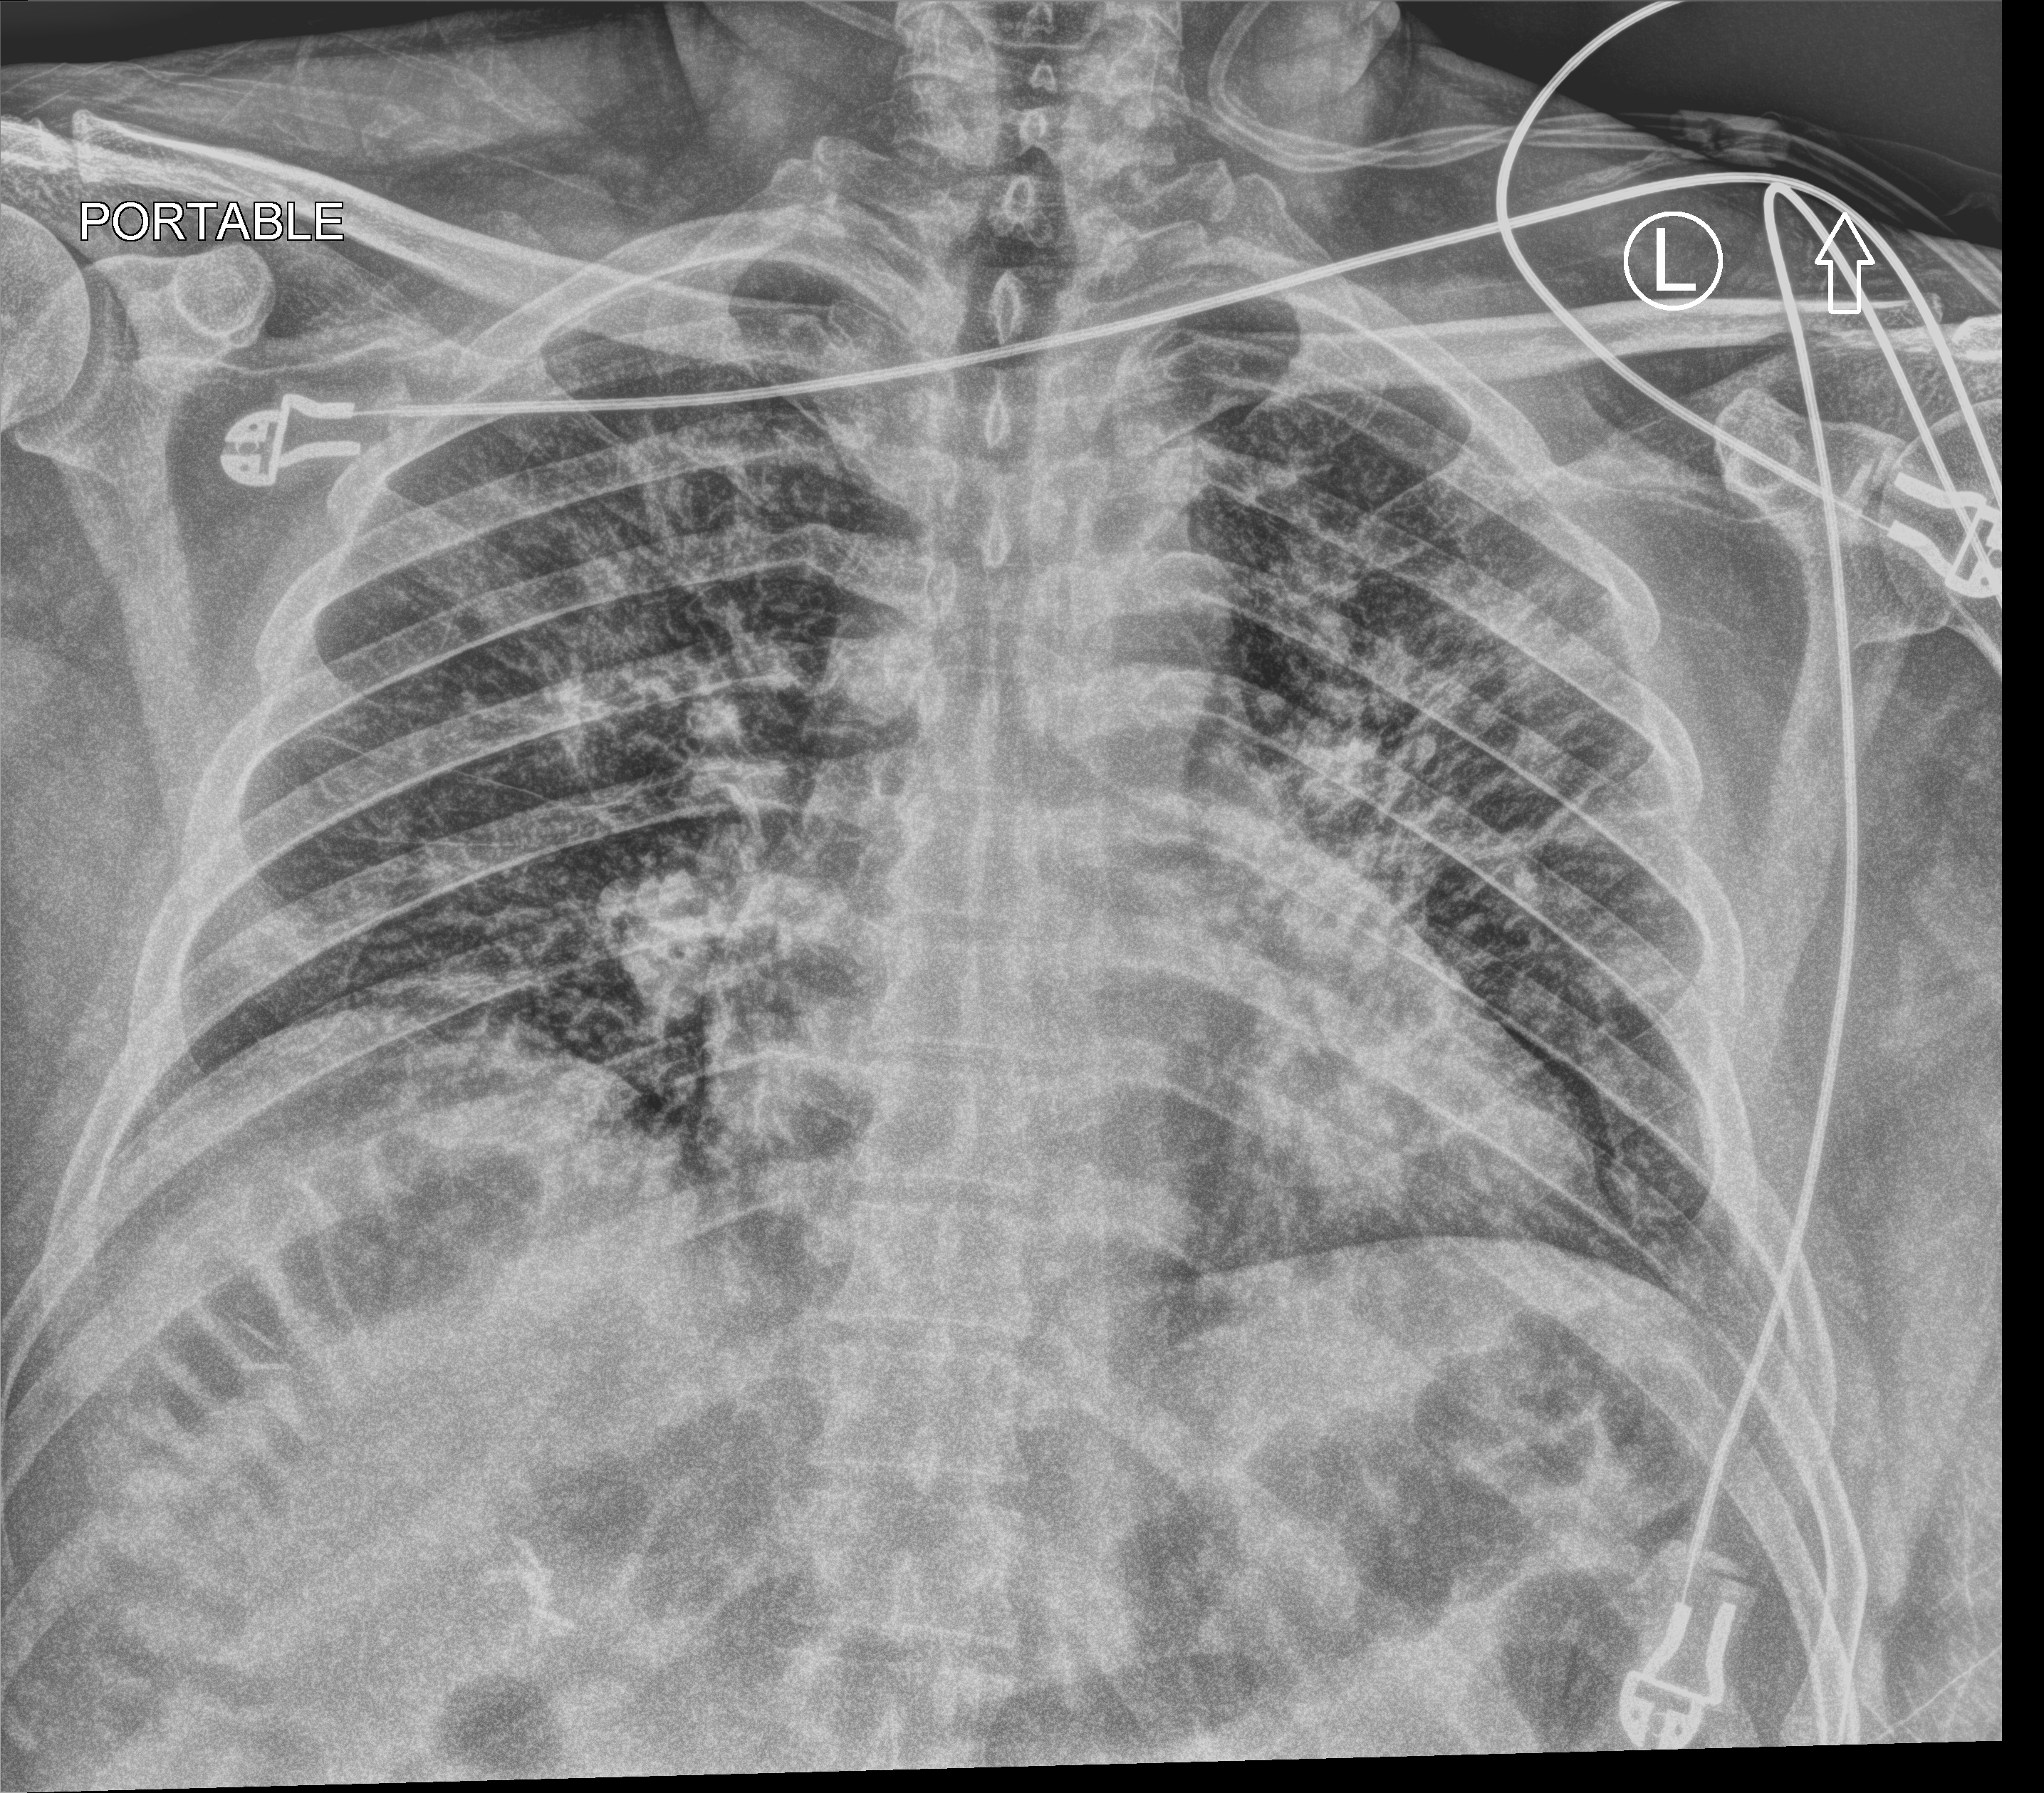
Bedside chest radiograph (computed radiography), anteroposterior (AP) projection. Male patient hospitalised with COVID-19, age 18–59 years.
Admission-level facts for this patient (not findings on this image; timing relative to this image not recorded):
- other chronic lung disease (admission record): no
- admitted to intensive care during this hospital stay: no
- mechanically ventilated during this hospital stay: no